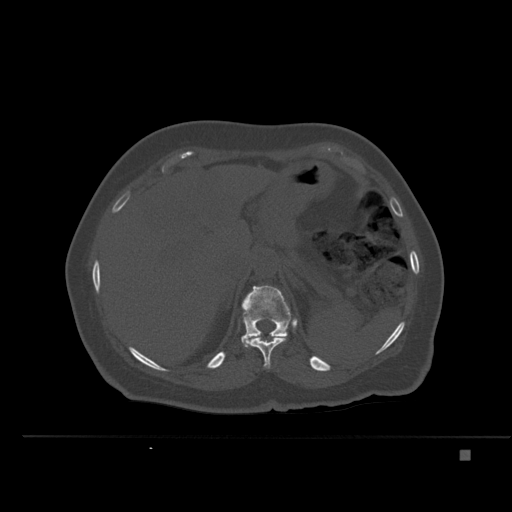
CT including the spine, one axial slice; position 261 of 477 along the scan axis; bone window (W 1800 / L 400 HU); 512 × 512 image matrix, field of view 422 × 422 mm. Patient: female, 74 years. From the clinical record (not read from this slice): primary cancer: colon.
Outlined on this slice (semi-automatically segmented with operator editing):
- T11 vertebra: bounding box [x1, y1, x2, y2] px = [246, 336, 287, 369]
- T12 vertebra: [241, 285, 292, 347]